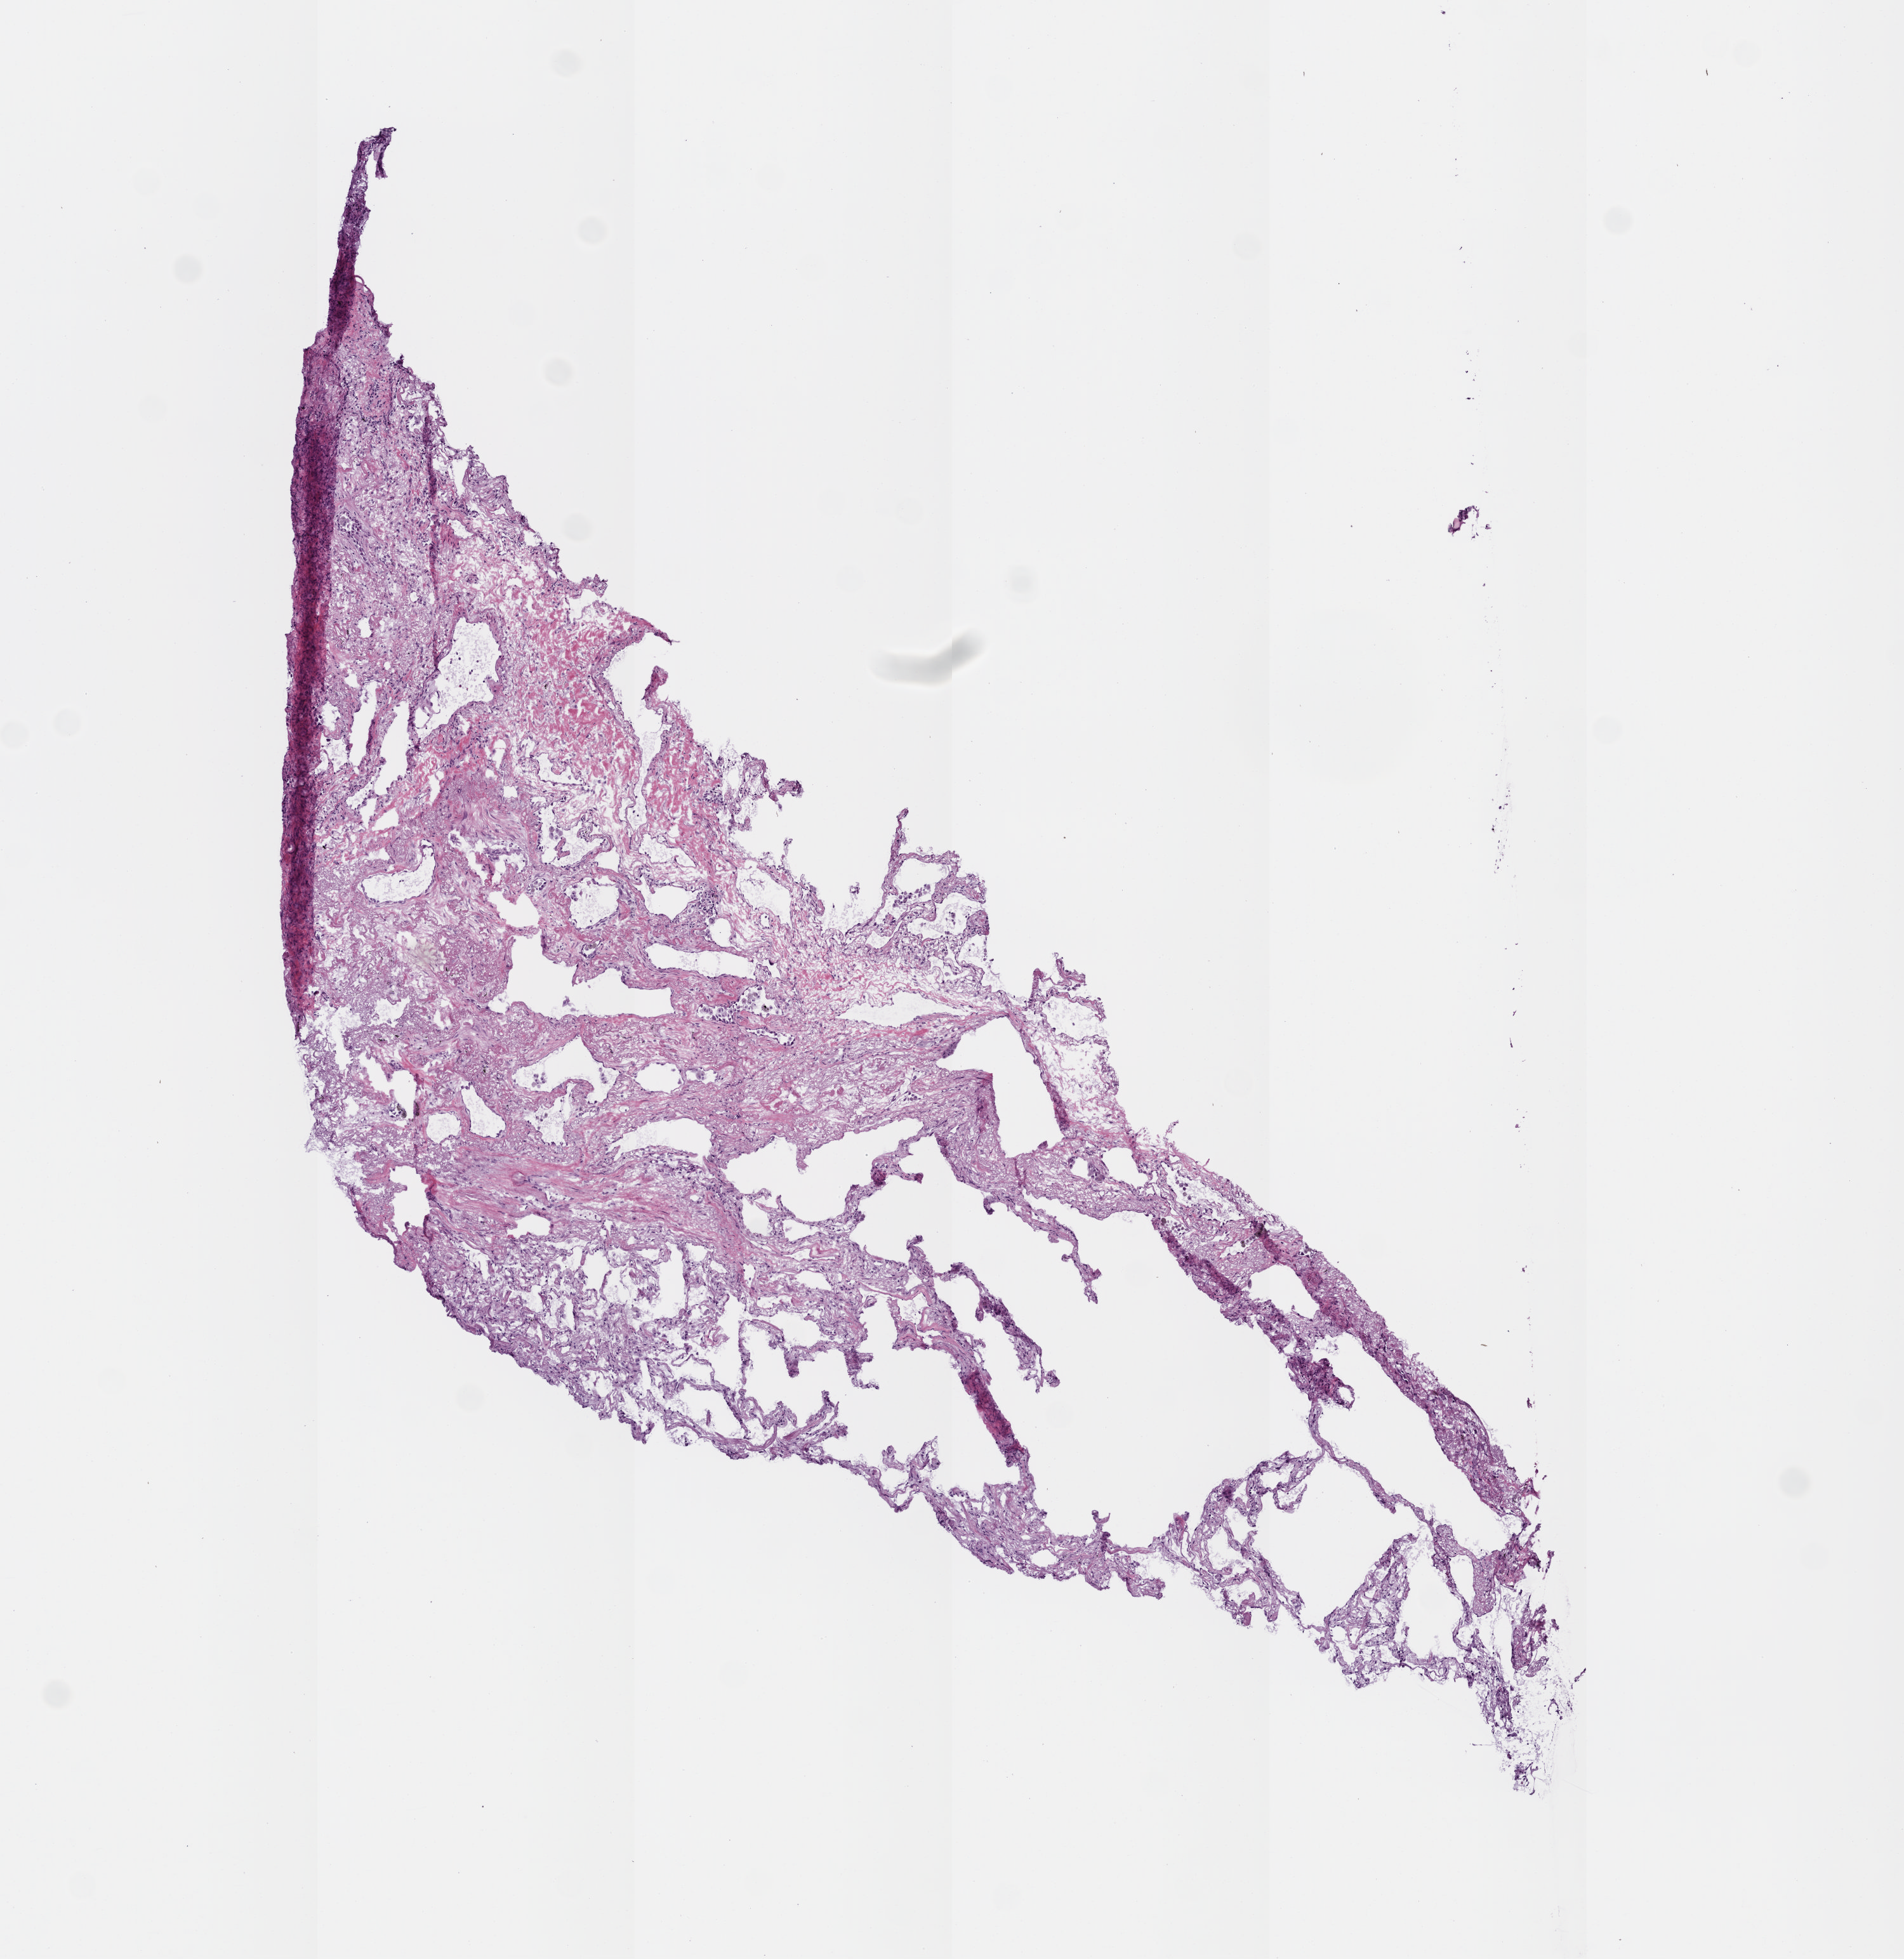
H&E whole-slide image — shown as a low-resolution overview of the whole scanned area (about 6.0 x 6.2 mm, acquisition: 20x scan), frozen section from the top of the tissue portion, sample: solid tissue normal (non-tumour tissue), lung. Female, age 69 years at initial diagnosis.
This section: solid tissue normal sample (biorepository sample class). Patient diagnosis: Adenocarcinoma, NOS (upper lobe, lung).